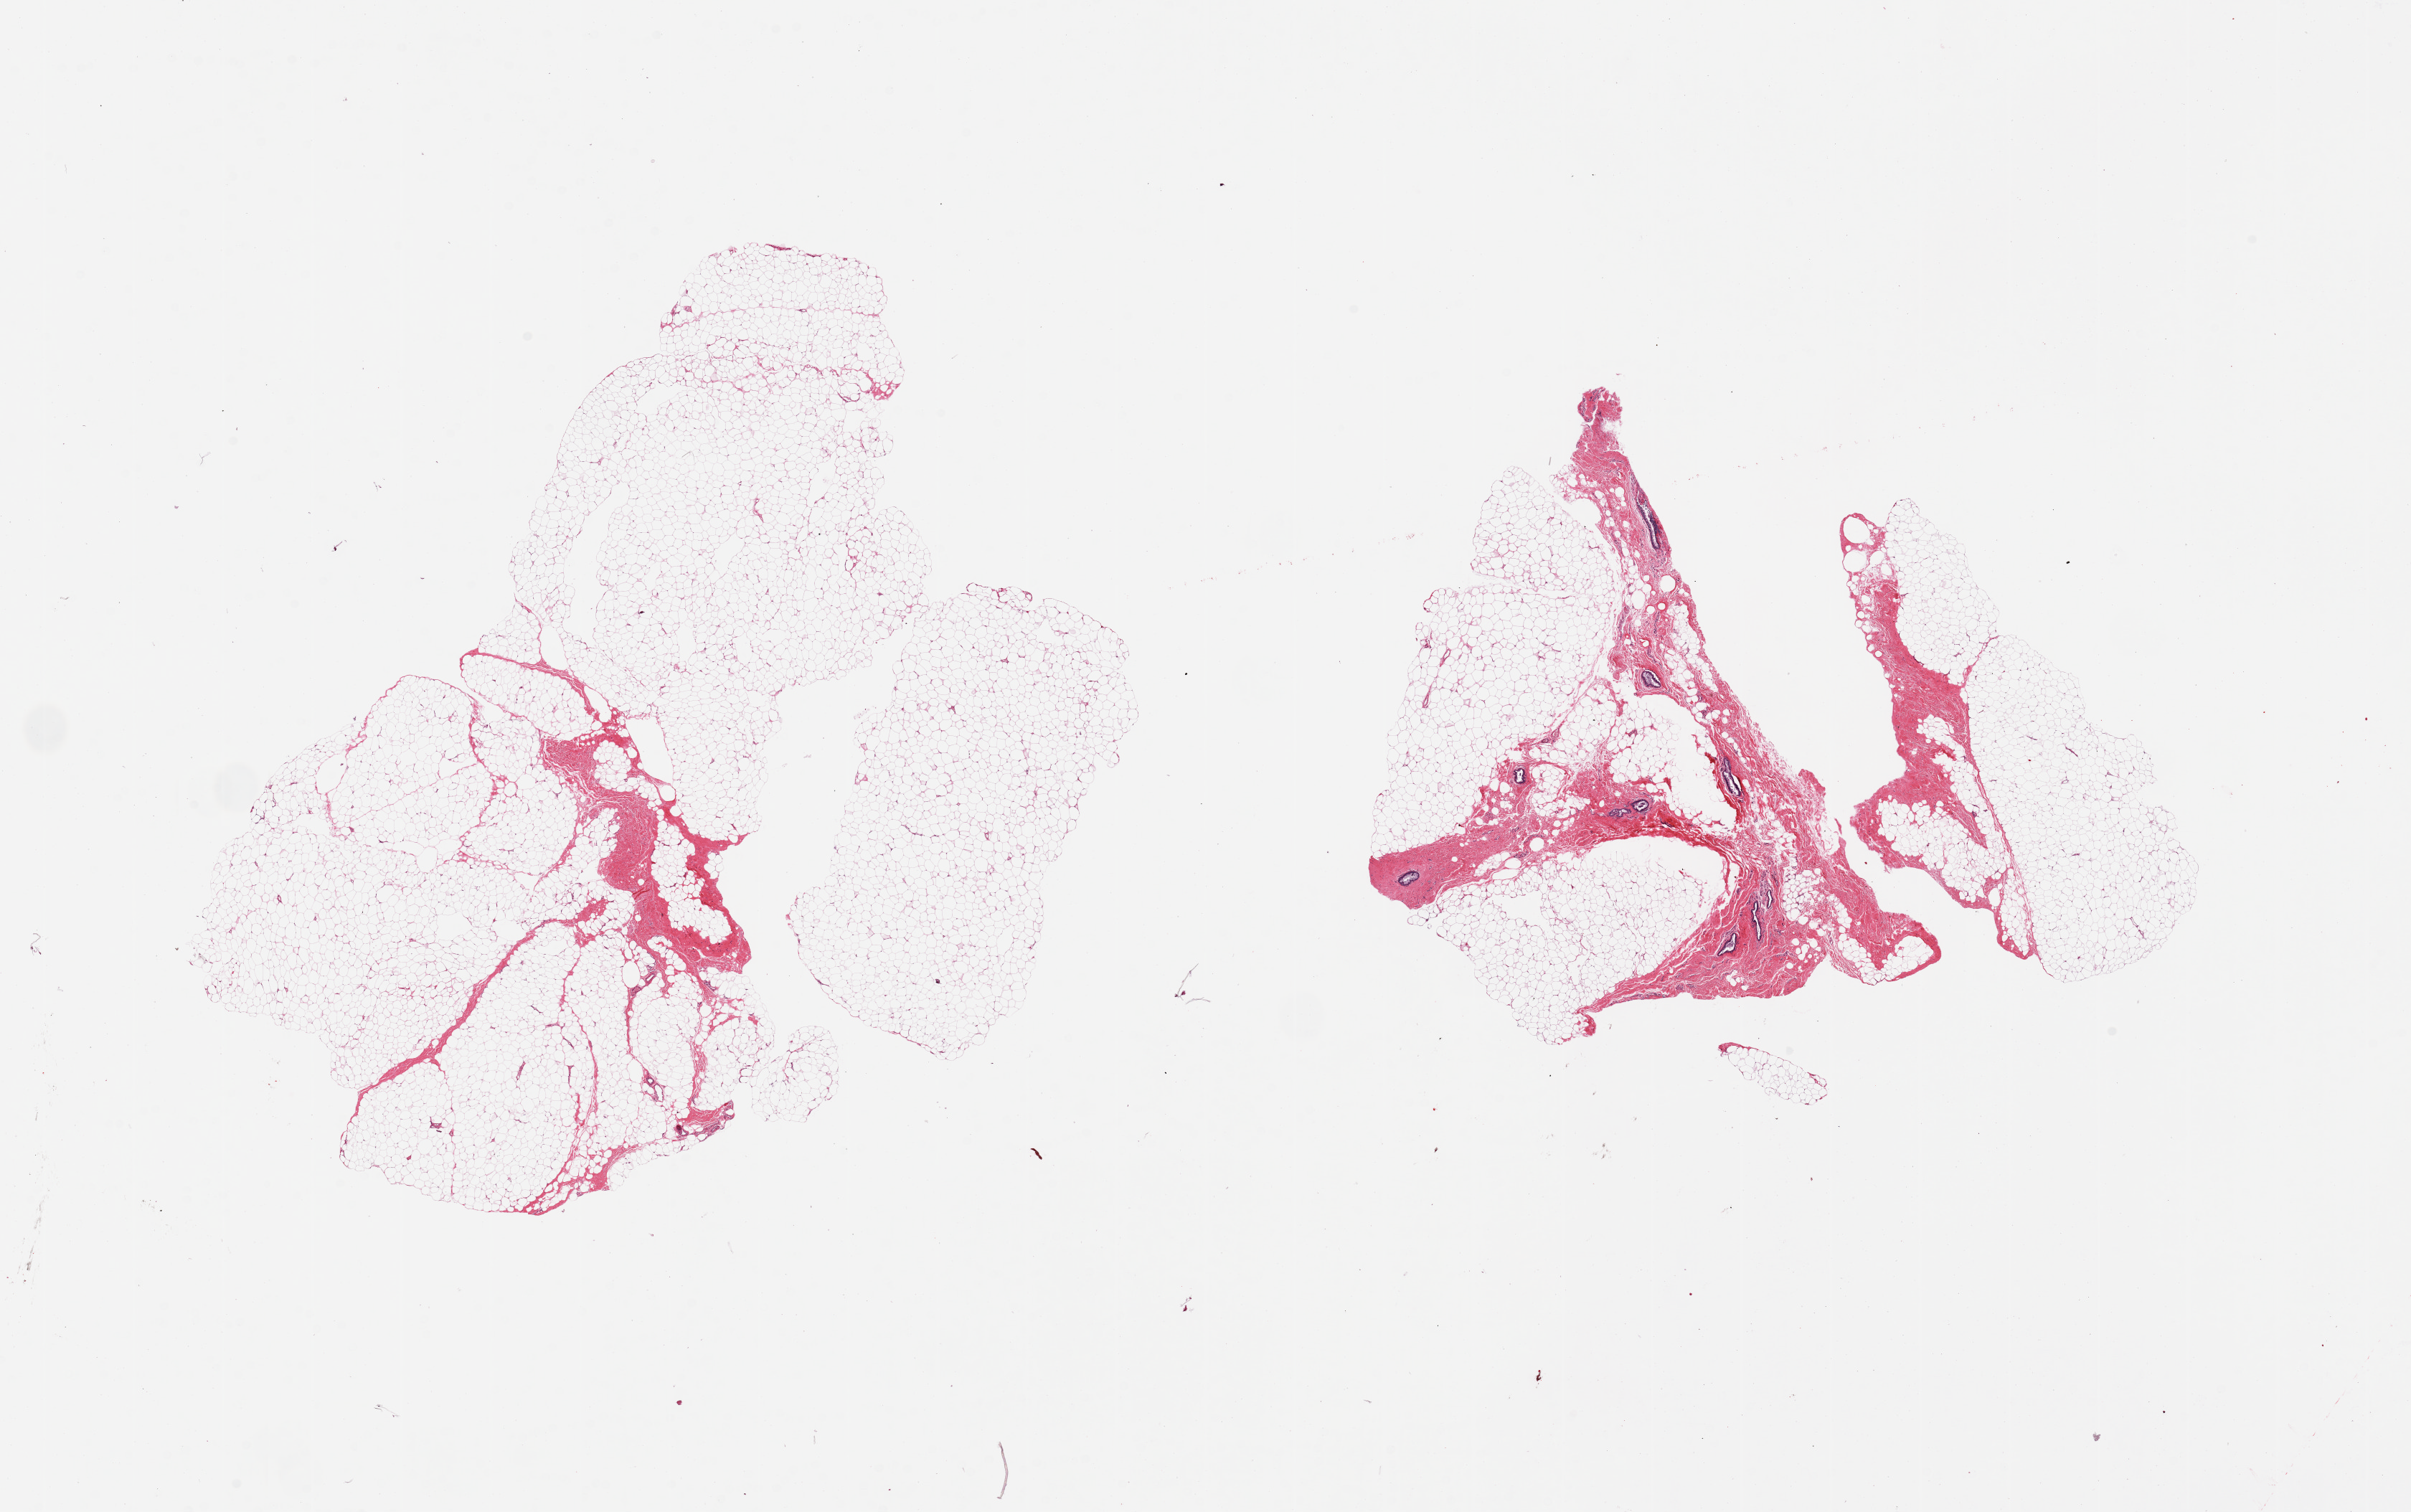
Haematoxylin and eosin whole-slide image — whole scanned area (about 26.6 x 16.7 mm, slide scanned at 20x) shown as a low-resolution overview; PAXgene-fixed paraffin-embedded (PFPE) section; section of breast (target tissue); donor tissue sample. Donor sex: male.
Review note (as recorded): 2 pieces. Fibroadipose tissue with several mammary ducts in one piece.